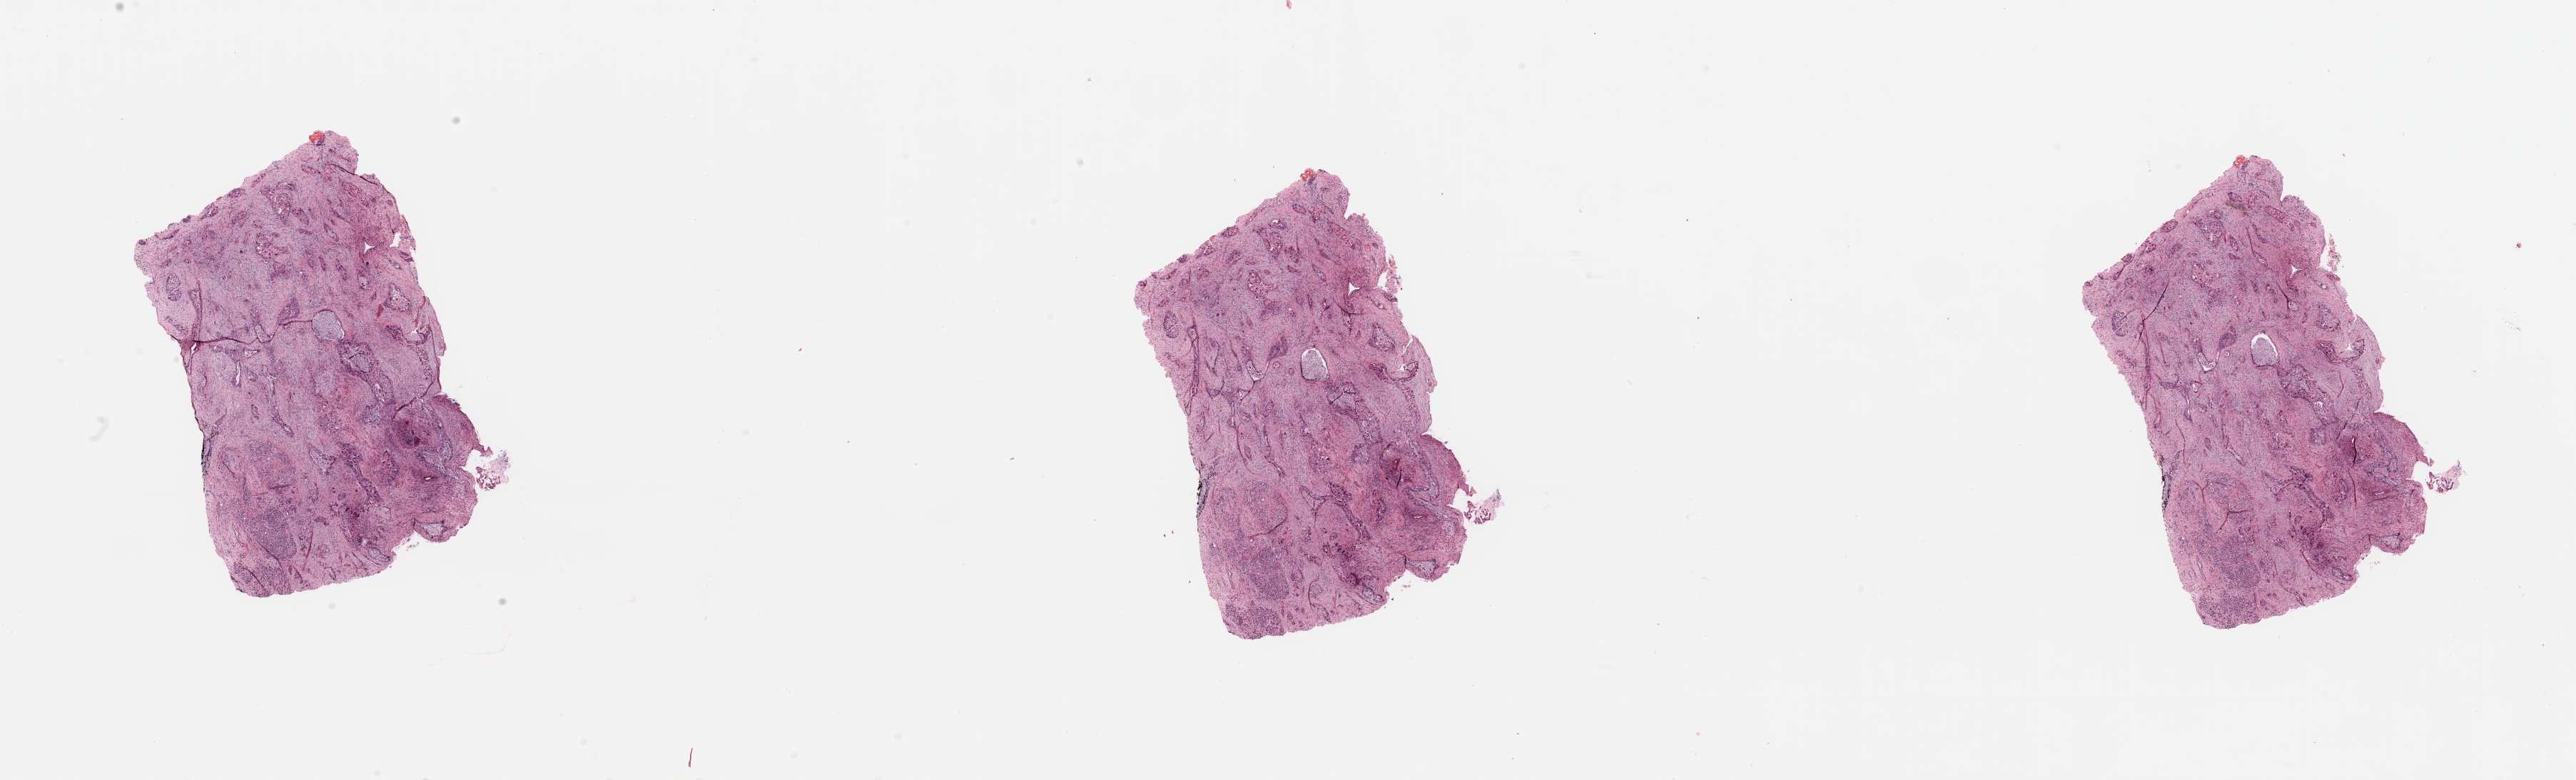
H&E whole-slide image — whole scanned area (about 28.5 x 8.6 mm, from a 20x scan) shown as a low-resolution overview. Tumour tissue sample, sampled site: pancreas. 68-year-old female patient. Histologic grade: G2 (moderately differentiated). Pathologist review of this section (percent, as recorded): tumour nuclei 40%, necrosis 2%.
Primary tumour site (as recorded): head. AJCC pathologic stage: IIB. Diagnosis: Infiltrating duct carcinoma, NOS.